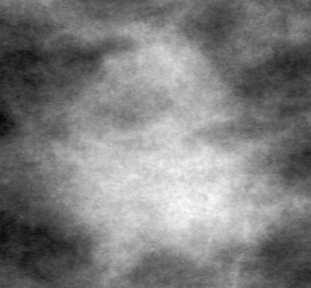
Crop from a digitized film mammogram around one marked abnormality, left breast, CC view, BI-RADS breast density category 2 (scale 1–4).
Finding: mass, shape irregular, margins ill defined; BI-RADS assessment category 4; pathology result (as recorded, not read from the image): malignant.